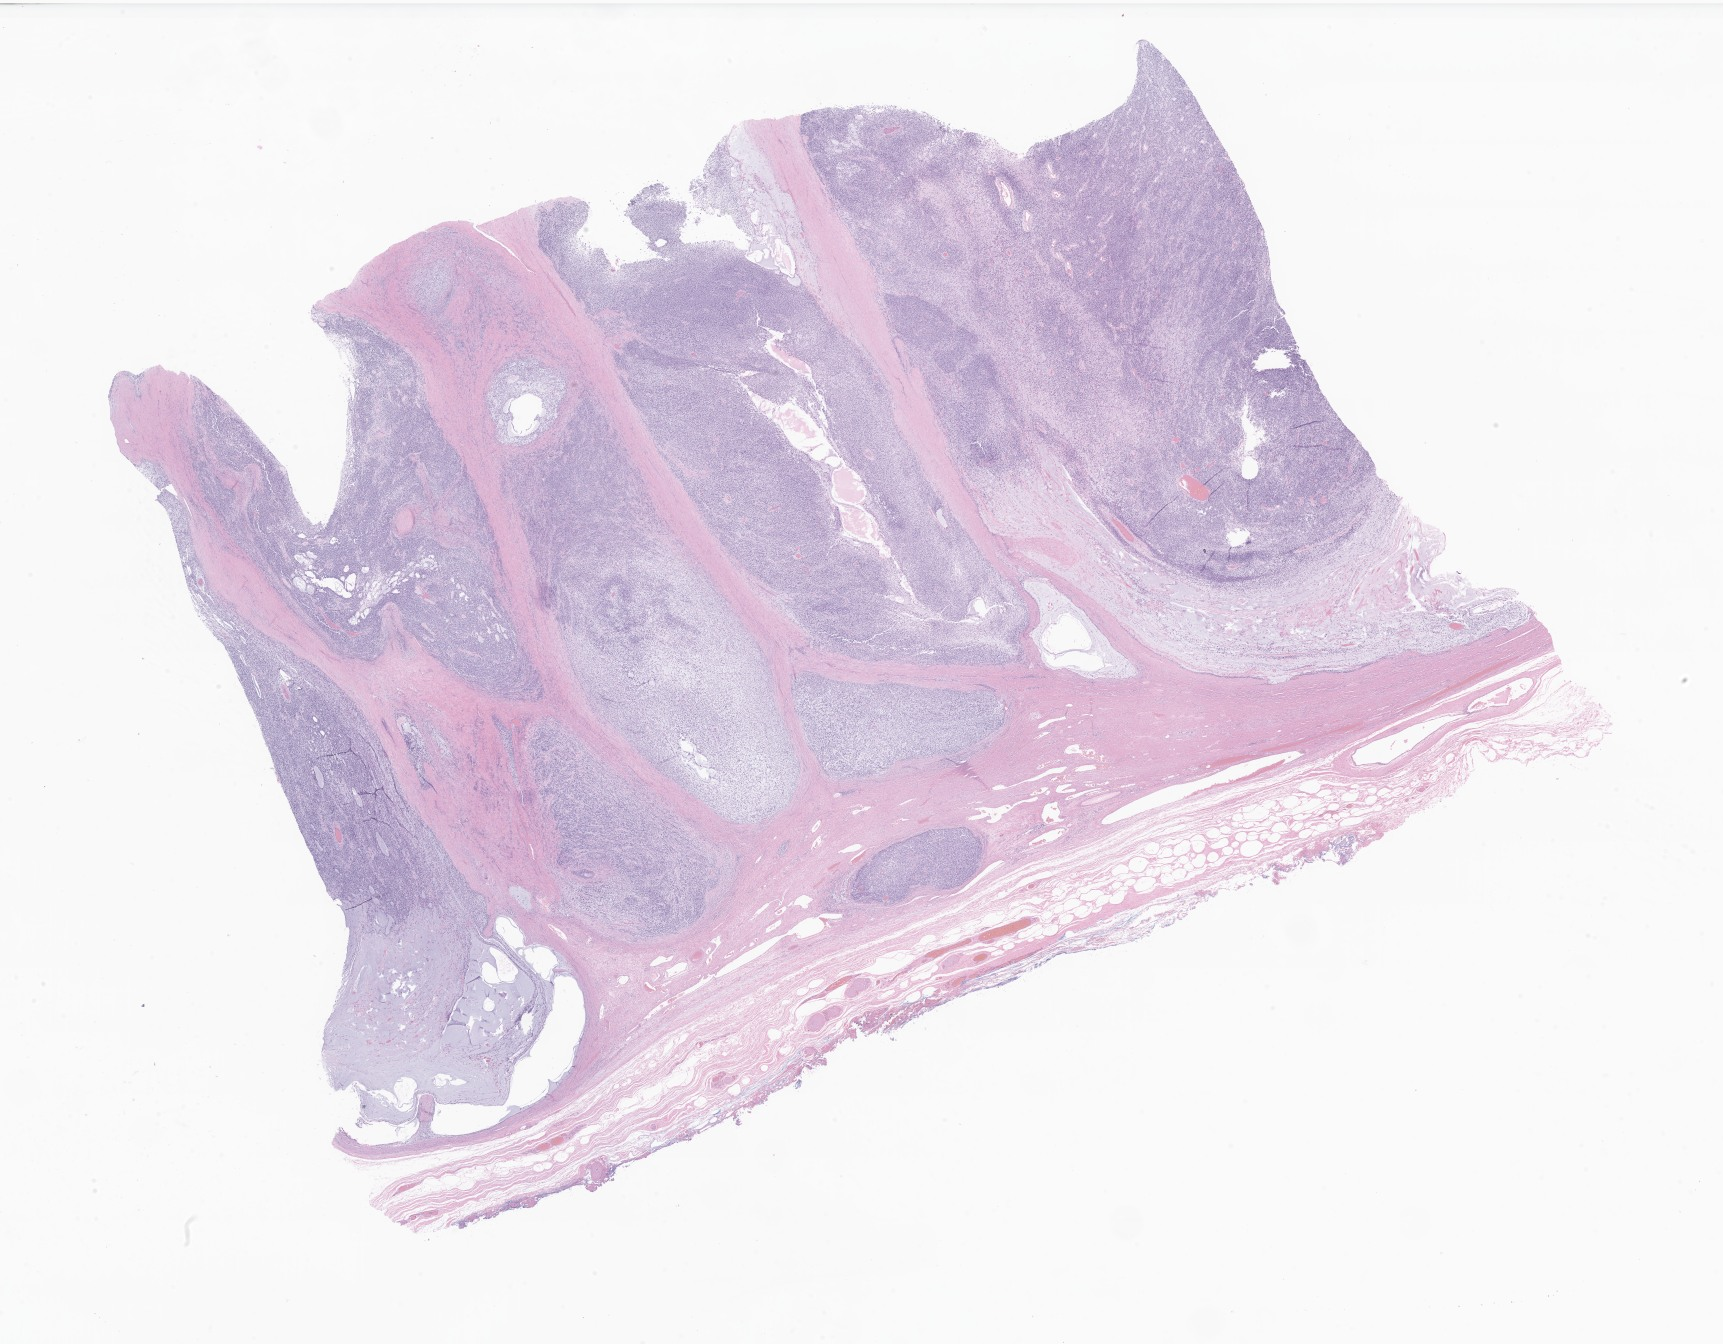
Hematoxylin and eosin (H&E) whole-slide image of tumor tissue from the testis — whole scanned area (about 29.1 x 22.7 mm) shown as a low-resolution overview. Formalin-fixed paraffin-embedded section. Male patient, age 237 months (19 years 9 months).
* recorded diagnosis: Rhabdomyosarcoma, NOS